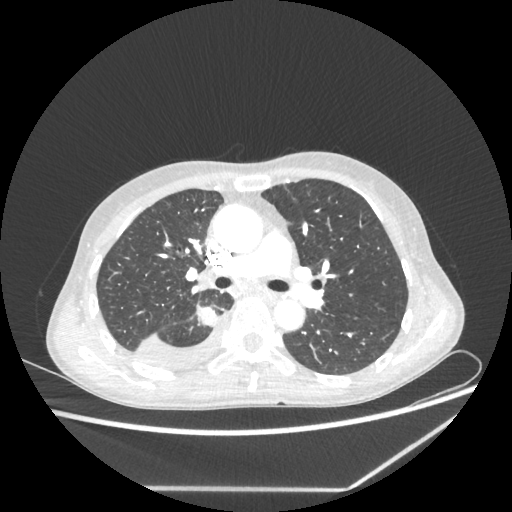
Chest CT, one axial slice; slice 142 of 237 in the series (ordered by position); reconstruction kernel STANDARD; 80 kVp; lung window (W 1500 / L -600 HU); 512 × 512 image matrix, field of view 364 × 364 mm. Female patient, age 59 years. From the clinical record (not read from this slice): clinical TNM (as recorded): T1c N1 M1.
Structures marked on this image (rectangle marked by the reading radiologist):
- lung tumour (recorded histology: adenocarcinoma): bounding box [x1, y1, x2, y2] px = [195, 303, 220, 329]